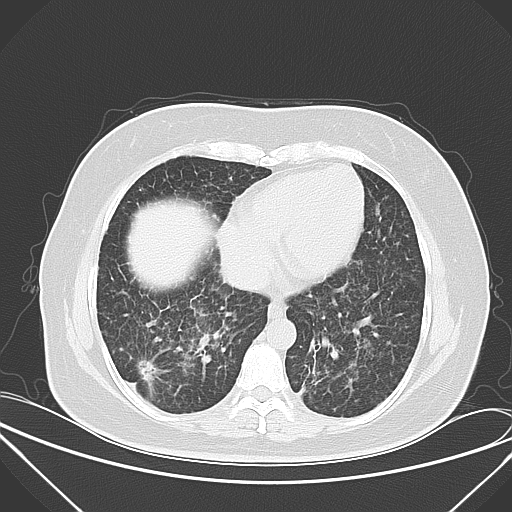
Chest CT, one axial slice; position 17 of 52 along the scan axis; 120 kVp; lung window (W 1500 / L -600 HU); 5 mm slice thickness; 512 × 512 image matrix, field of view 386 × 386 mm. Patient: female, 50 years. From the clinical record (not read from this slice): clinical TNM (as recorded): T1c N0 M1a.
Annotated regions visible in this slice (bounding box drawn by a radiologist):
- lung tumour (recorded histology: adenocarcinoma): bounding box [x1, y1, x2, y2] px = [132, 356, 166, 394]